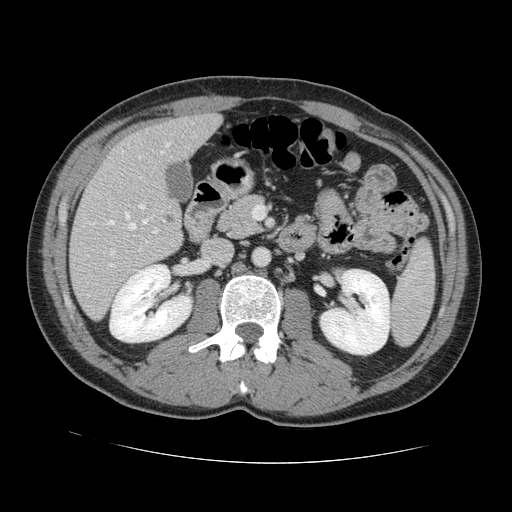
Contrast-enhanced abdominal CT, one axial slice; slice 60 of 131 in the series (ordered by position); 120 kVp; intravenous contrast given; soft-tissue window (W 400 / L 40 HU); 2.5 mm slice thickness; 512 × 512 image matrix, field of view 380 × 380 mm. Male patient, age 40 years. Case-level facts recorded for this patient, not image findings: diagnosis: colorectal cancer liver metastases, imaged before liver resection; multiple liver metastases: yes; largest metastasis: 2.9 cm; disease in both lobes: yes.
Structures marked on this image (manually delineated by an expert):
- hepatic veins: box from (x=108, y=142) to (x=171, y=255) px
- liver: (x=71, y=115)–(x=219, y=318)
- planned liver remnant (the part of the liver to remain after resection): (x=112, y=115)–(x=219, y=178)
- portal vein (with intrahepatic branches): (x=109, y=156)–(x=158, y=267)
- liver metastasis: (x=165, y=216)–(x=175, y=225)